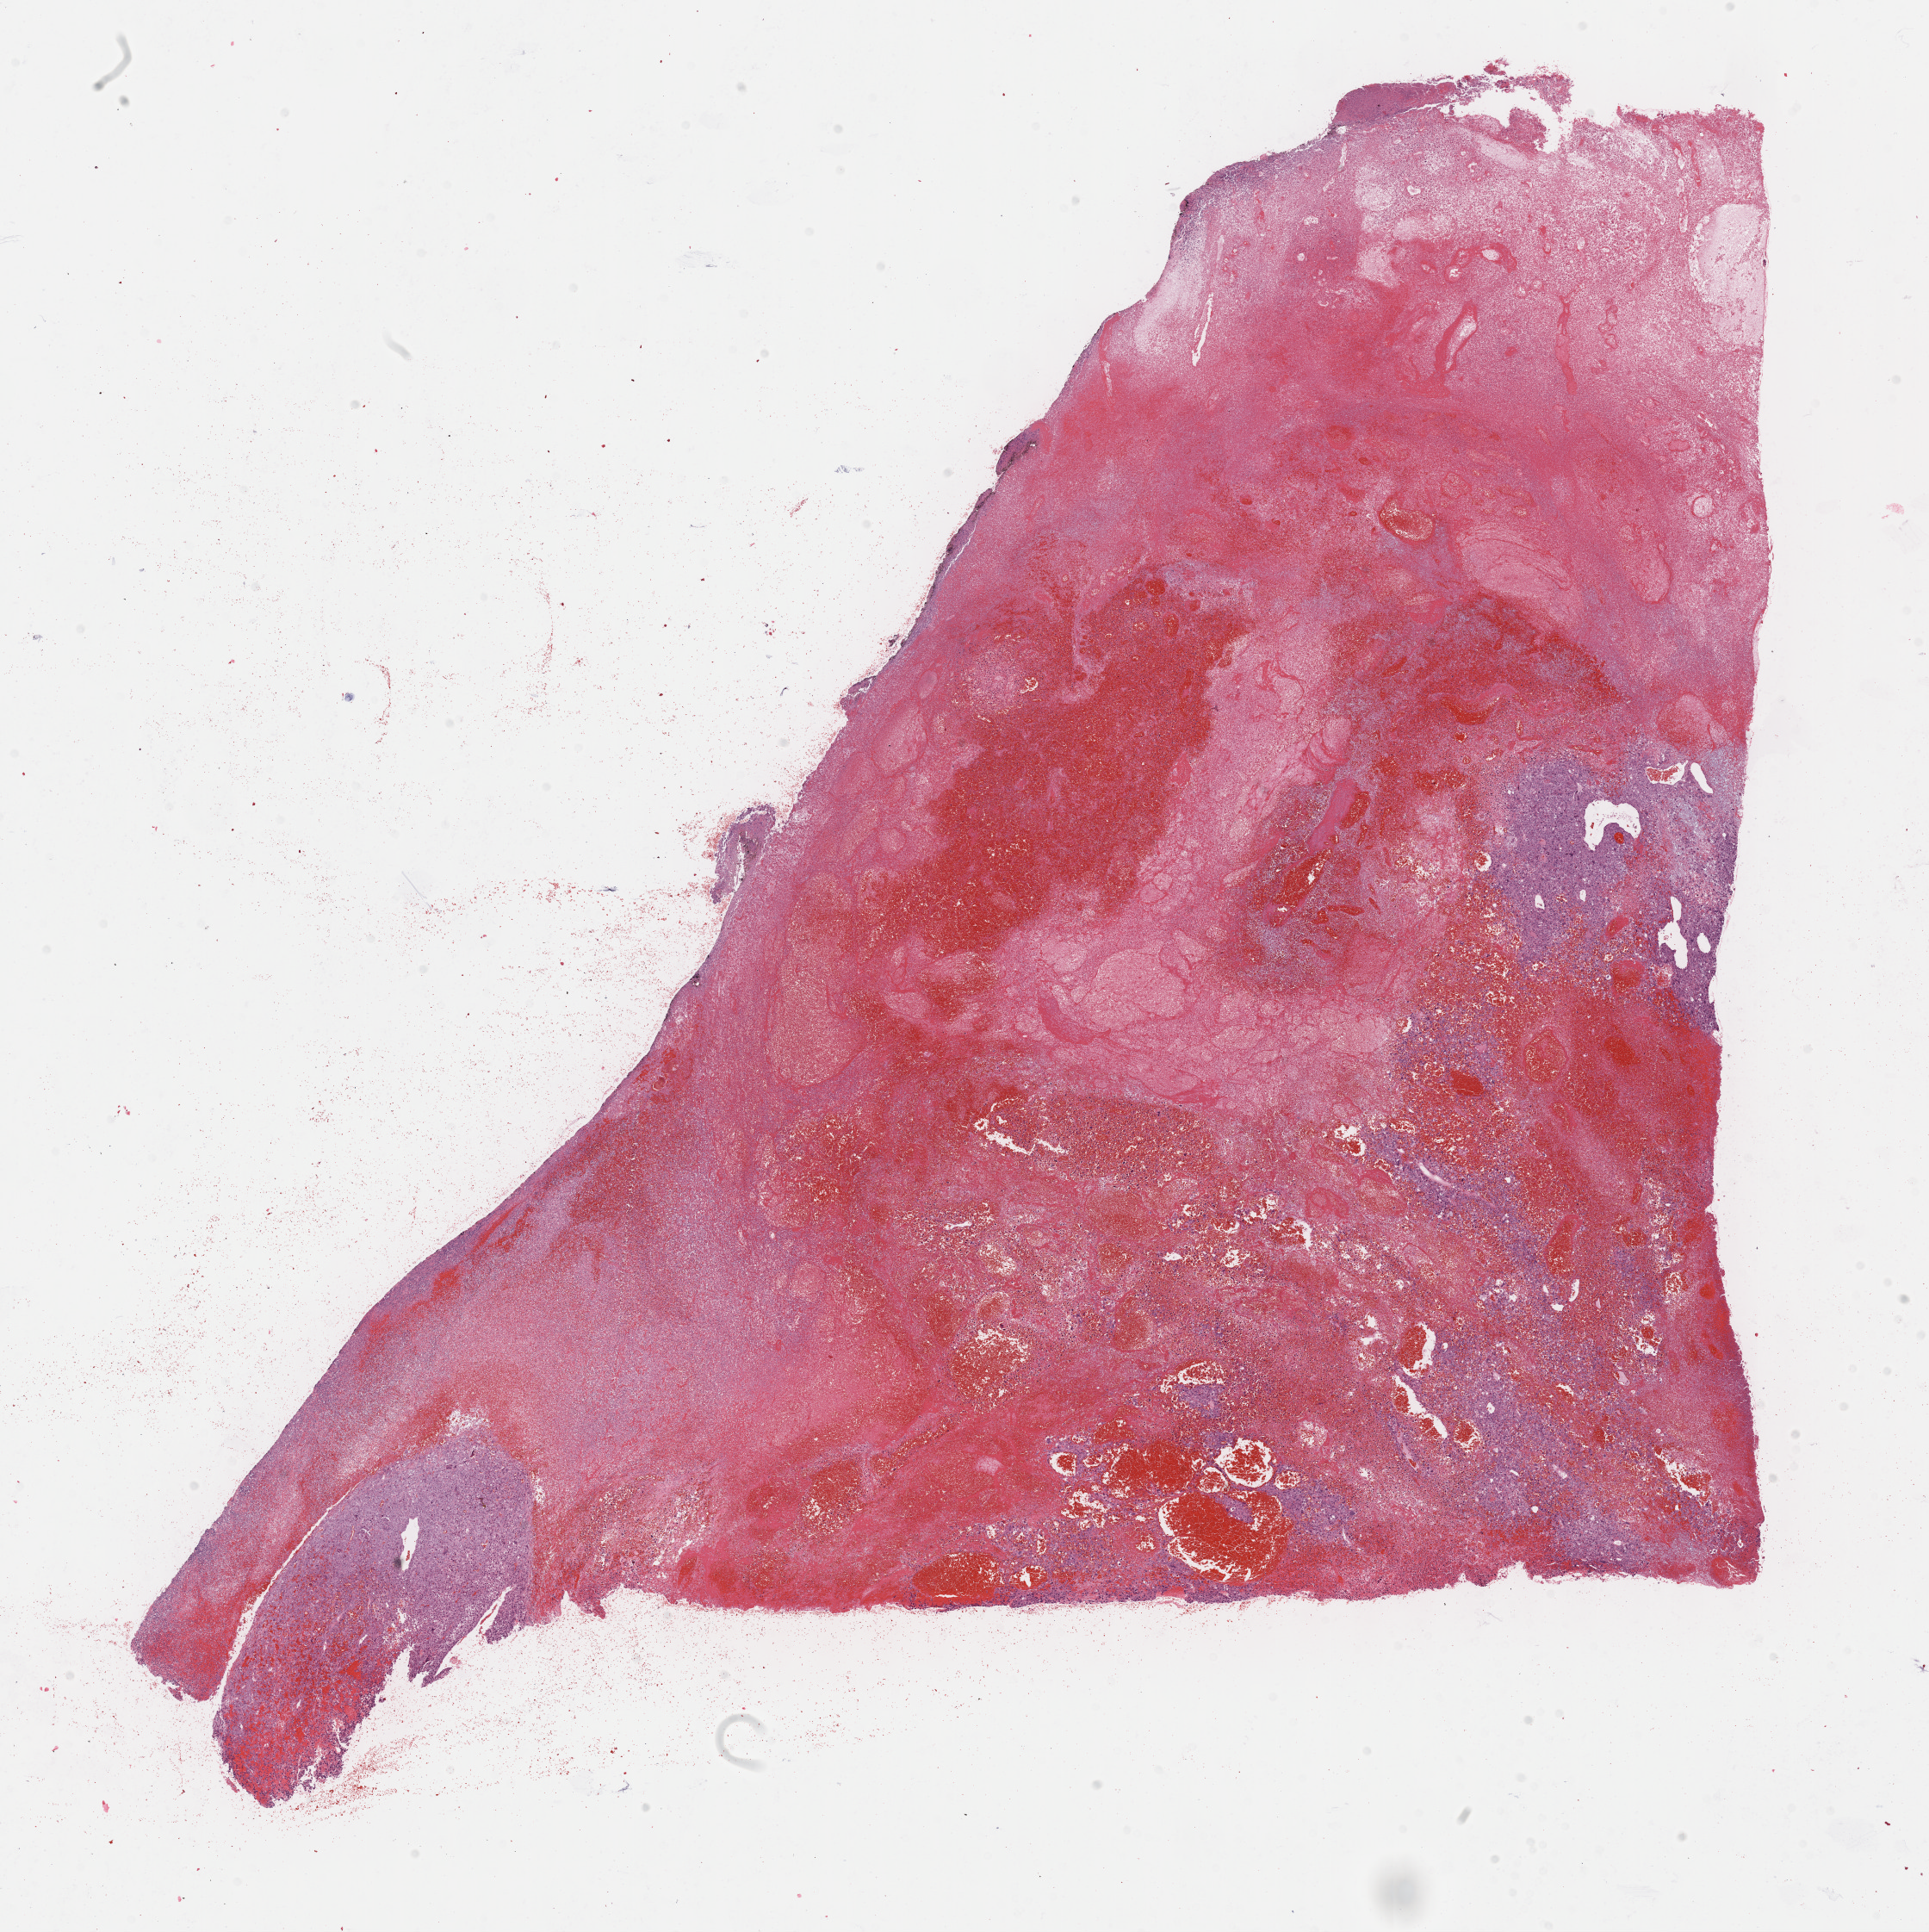
Digitized Hematoxylin and eosin (H&E) stained tissue section (whole slide), whole scanned area (about 18.1 x 18.1 mm) shown as a low-resolution overview, formalin-fixed paraffin-embedded (FFPE) diagnostic section, bladder, primary tumour sample. Male patient; age at initial diagnosis 68 years.
Pathologic diagnosis: Papillary transitional cell carcinoma.